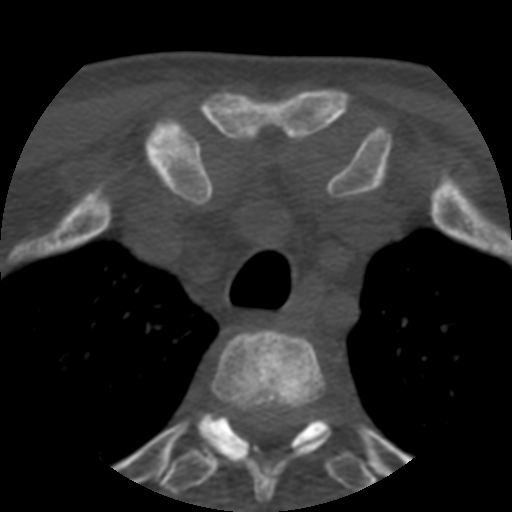
CT including the spine, one axial slice. Position 424 of 508 along the scan axis. Reconstruction kernel STANDARD. 120 kVp. Bone window (W 1800 / L 400 HU). 1.25 mm slice thickness. 512 × 512 image matrix. Patient age 57 years. Case-level facts recorded for this patient, not image findings: primary cancer: prostate.
Annotated regions visible in this slice (semi-automatically segmented with operator editing):
- T2 vertebra: box from (x=200, y=329) to (x=329, y=503) px
- T3 vertebra: (x=160, y=414)–(x=375, y=496)